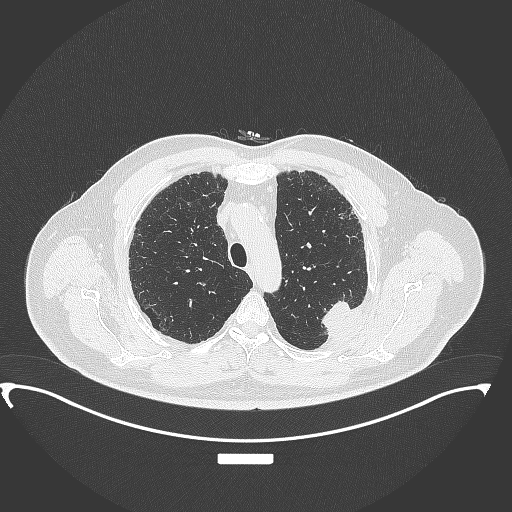
Chest CT, one axial slice. Slice 278 of 350 in the series (ordered by position). Reconstruction kernel B70f. Lung window (W 1500 / L -600 HU). 512 × 512 image matrix, field of view 459 × 459 mm. Patient: male, 64 years. From the clinical record (not read from this slice): clinical TNM (as recorded): T1c N1 M1.
Annotated regions visible in this slice (rectangle marked by the reading radiologist):
- lung tumour (recorded histology: adenocarcinoma): bounding box <314,295,357,343> (left, top, right, bottom; pixels)